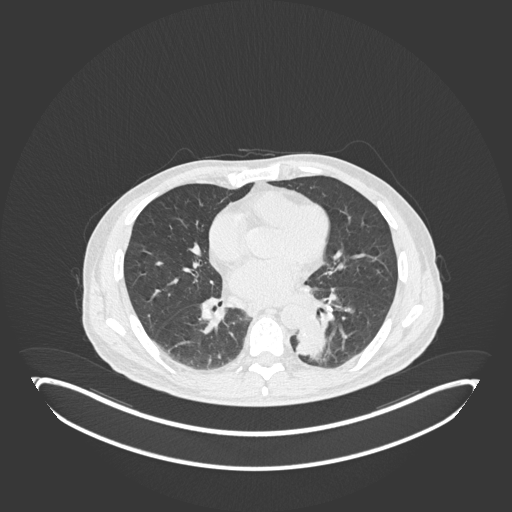
Chest CT, one axial slice; position 80 of 251 along the scan axis; reconstruction kernel B30f; 120 kVp; lung window (W 1500 / L -600 HU); 512 × 512 image matrix, field of view 500 × 500 mm. Male patient, age 72 years. Case-level facts recorded for this patient, not image findings: clinical TNM (as recorded): T2b N0 M1.
Annotated regions visible in this slice (bounding box drawn by a radiologist):
- lung tumour (recorded histology: adenocarcinoma): bounding box [x1, y1, x2, y2] px = [294, 317, 330, 359]